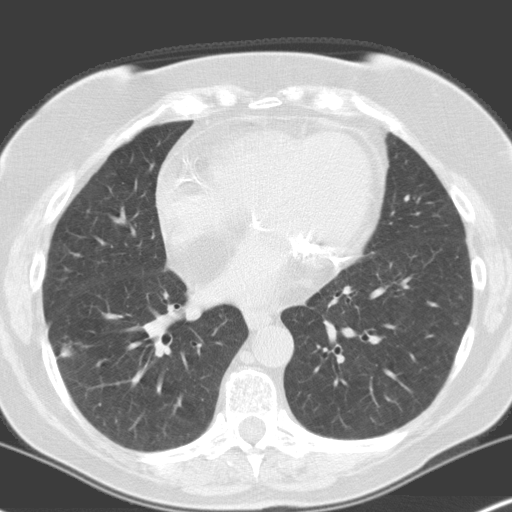
Low-dose screening chest CT, one axial slice; slice 75 of 160 in the series (ordered by position); 120 kVp; lung window (W 1500 / L -600 HU); 3.2 mm slice thickness; 512 × 512 image matrix, field of view 316 × 316 mm.
Annotated regions visible in this slice (expert manual segmentation):
- lesion 1 (tumor, lower lobe of right lung): bounding box <62,346,71,357> (left, top, right, bottom; pixels)